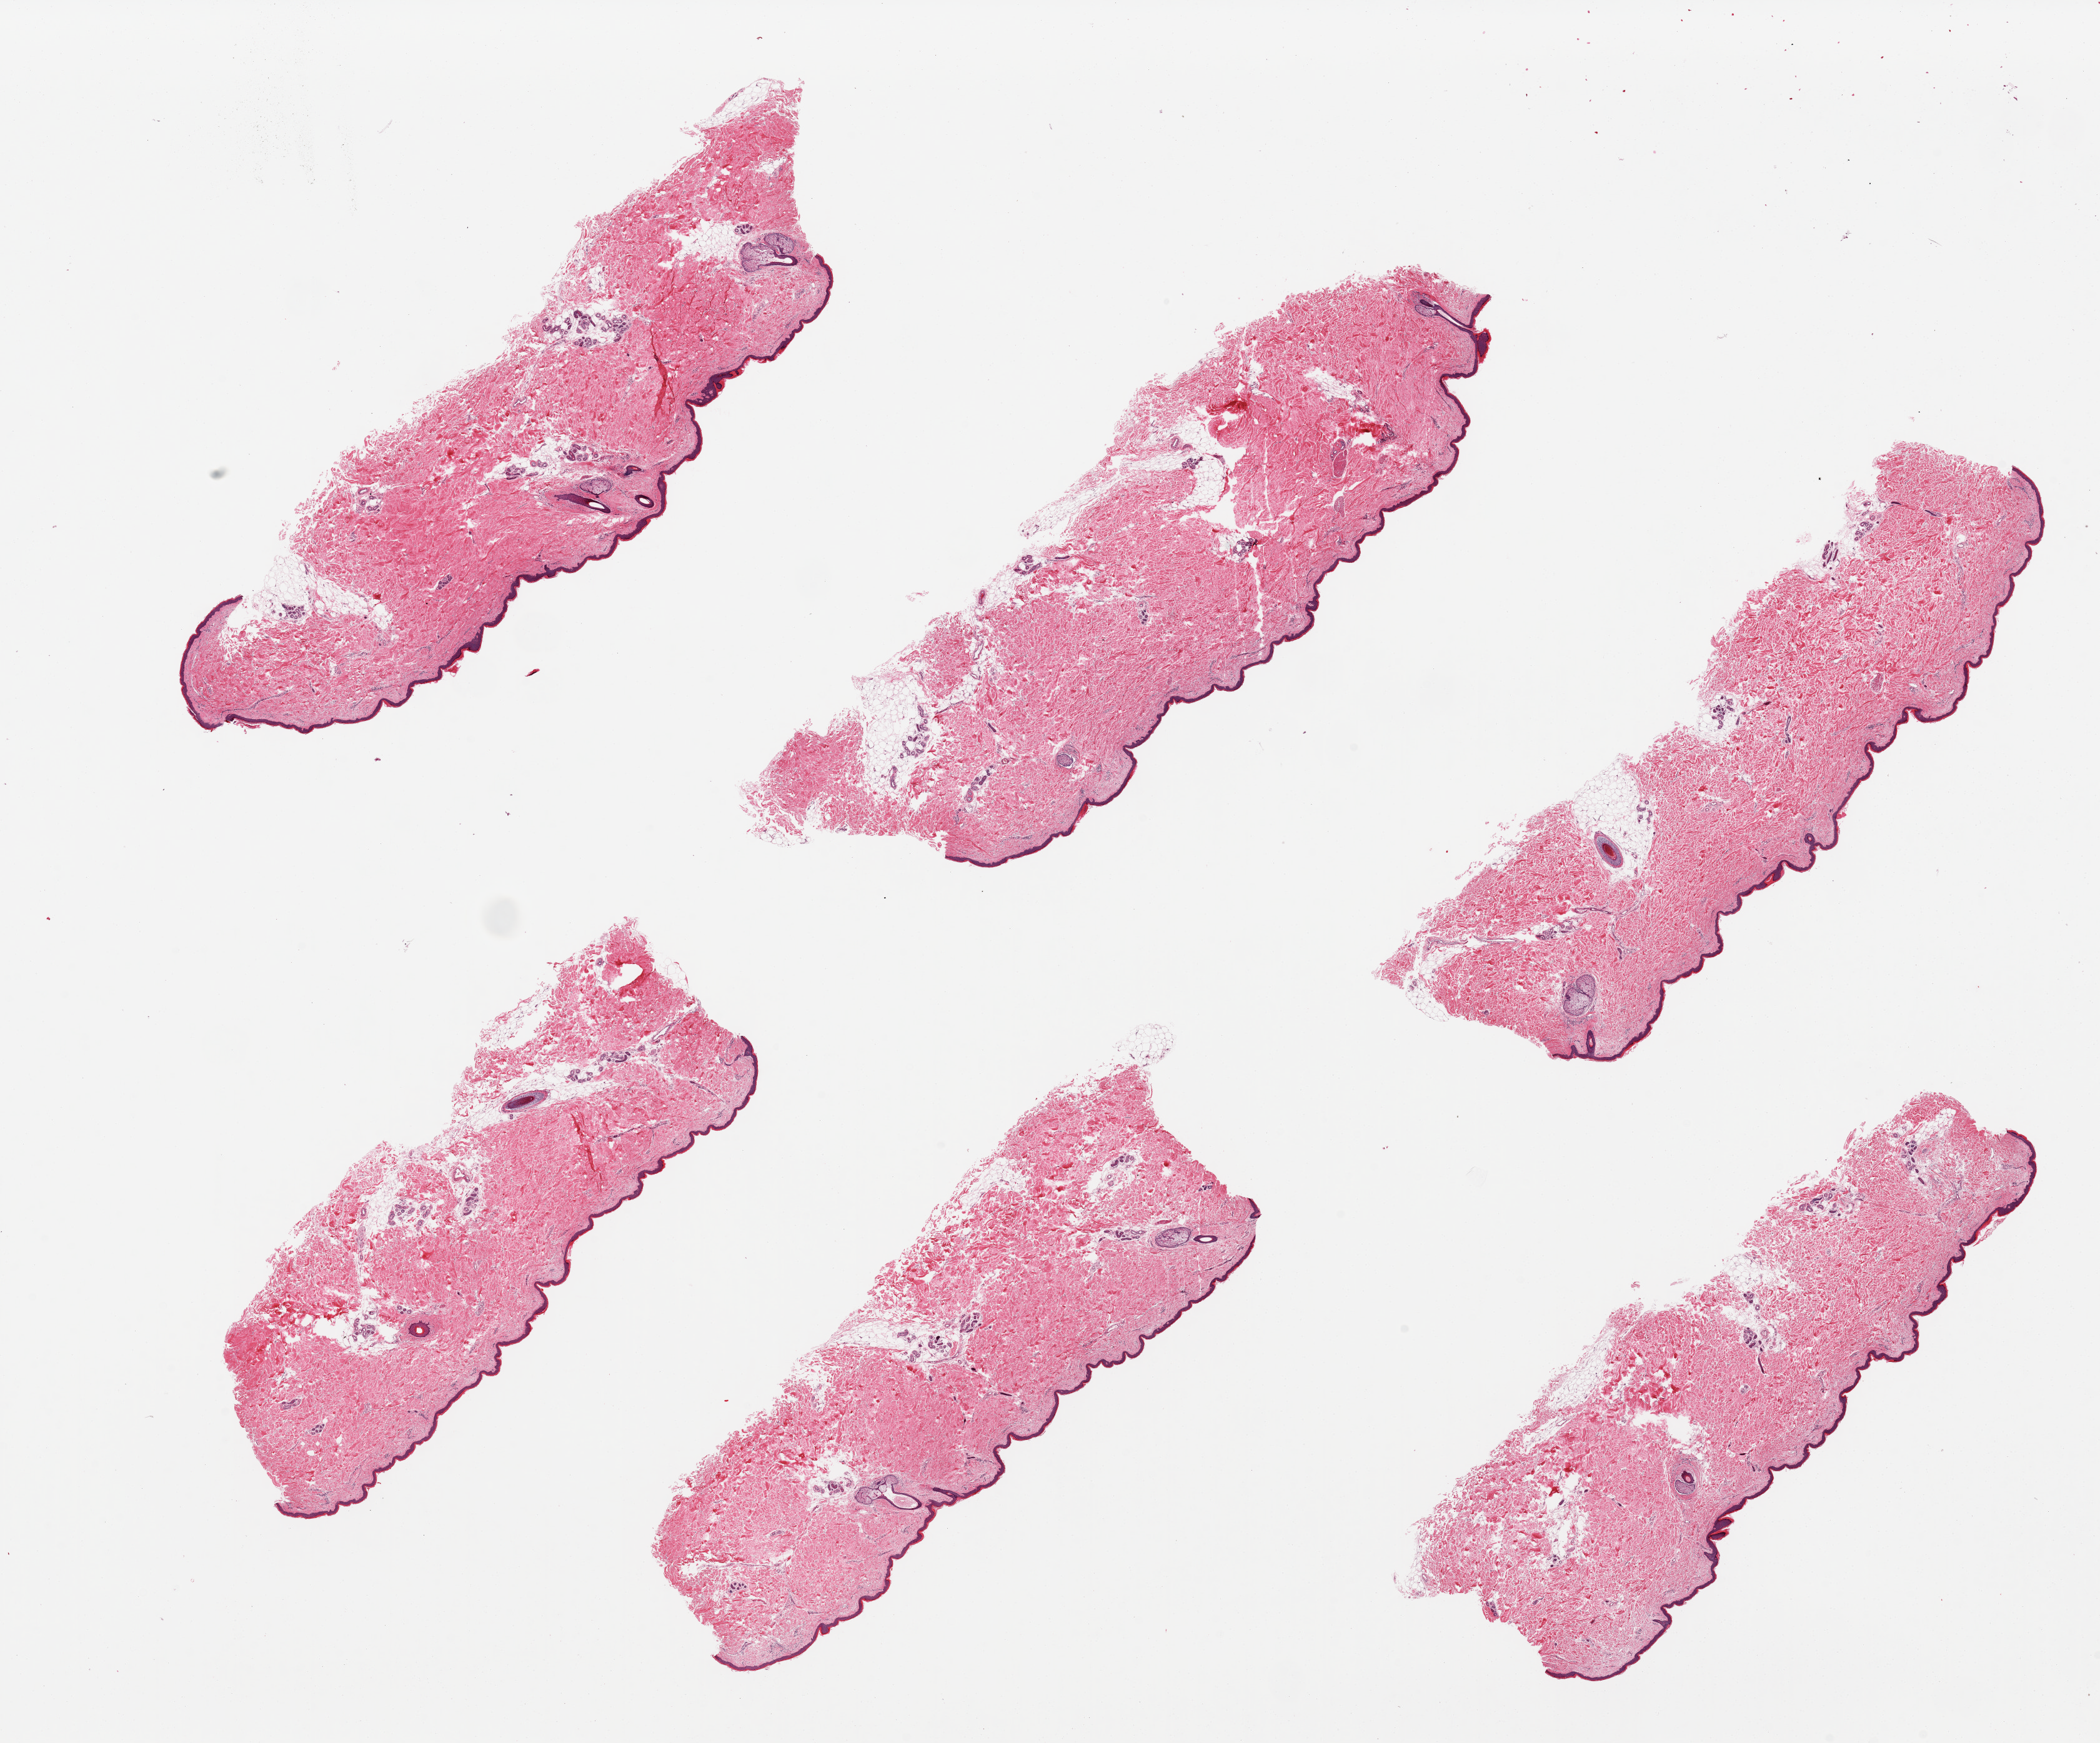
Whole-slide image, hematoxylin and eosin (H&E) stain, shown as a low-resolution overview of the whole scanned area (about 26.6 x 22.1 mm). PAXgene-fixed, paraffin-embedded tissue. Target tissue: skin of lower leg. Donor tissue sample. Male donor.
Reviewer comment on this tissue sample: 6 pieces, well-trimmed, squamous epithelium is about 1.5-2% of thickness.